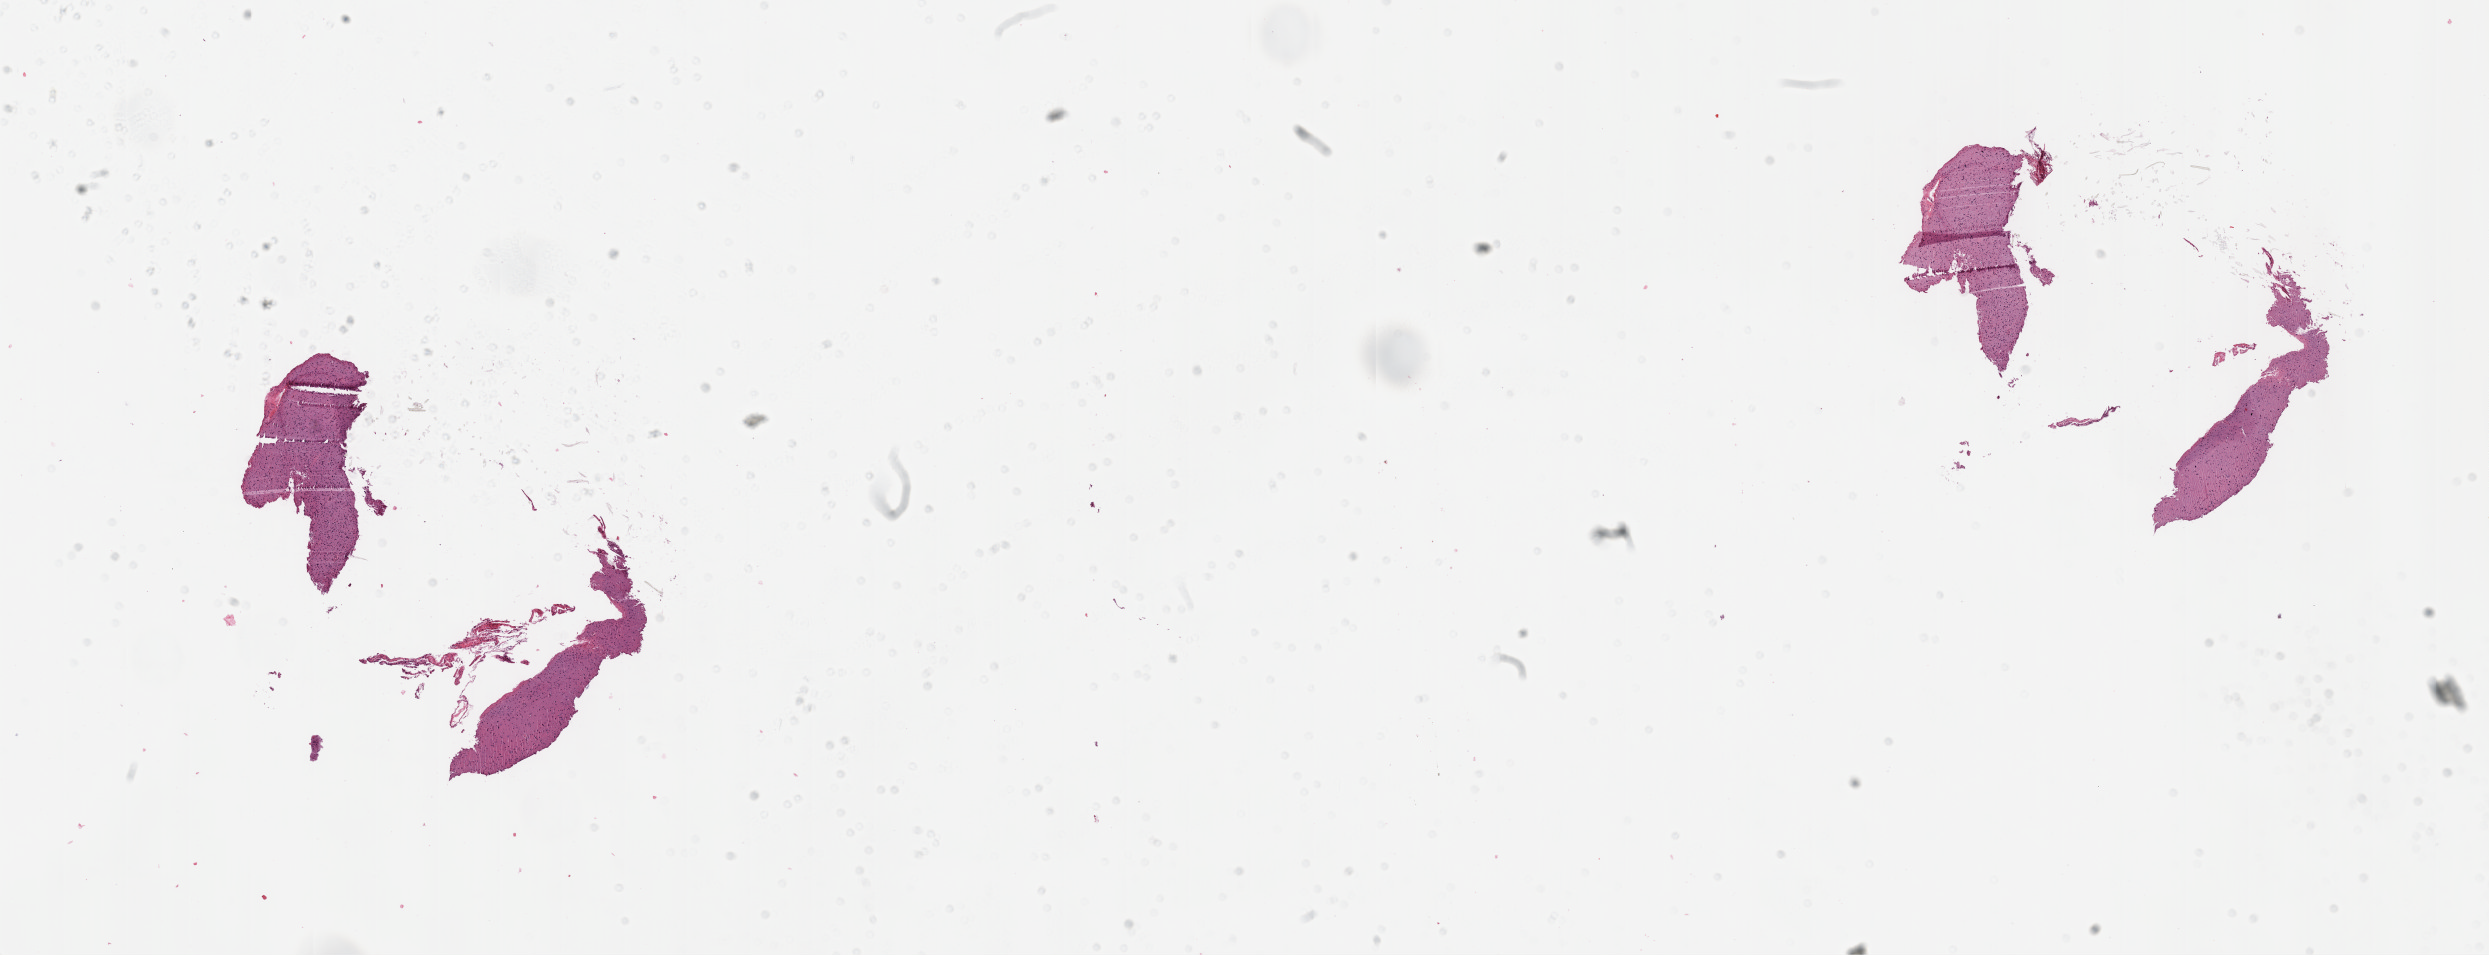
H&E-stained whole-slide image — shown as a low-resolution overview of the whole scanned area (about 20.1 x 7.7 mm, from a 40x scan); formalin-fixed paraffin-embedded (FFPE) diagnostic section; sample: primary tumour, brain. Male patient; age at initial diagnosis 37 years. Histologic grade: G3 (poorly differentiated).
- diagnosis: Oligodendroglioma, anaplastic
- laterality: right